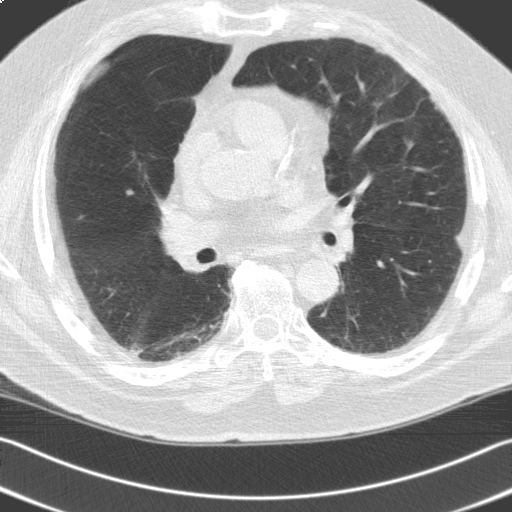
Low-dose screening chest CT, one axial slice; position 89 of 162 along the scan axis; 120 kVp; lung window (W 1500 / L -600 HU); 3.2 mm slice thickness; 512 × 512 image matrix, field of view 345 × 345 mm.
Structures marked on this image (outlined manually by an expert reader):
- lesion 1 (tumor, upper lobe of right lung): bounding box [x1, y1, x2, y2] px = [125, 187, 136, 198]